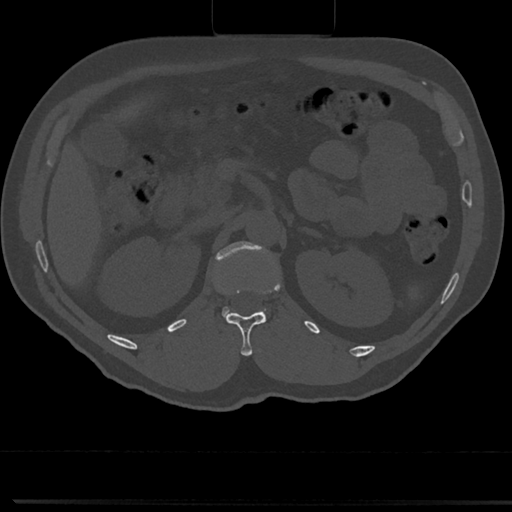
CT including the spine, one axial slice; position 119 of 817 along the scan axis; bone window (W 1800 / L 400 HU); 0.5 mm slice thickness; 512 × 512 image matrix. Patient: male, 61 years. Case-level facts recorded for this patient, not image findings: primary cancer: prostate.
Annotated regions visible in this slice (semi-automatic segmentation, software-assisted and operator-edited):
- L1 vertebra: bounding box (x1, y1, x2, y2) in pixels: (212, 241, 277, 322)
- T12 vertebra: (224, 311, 268, 355)